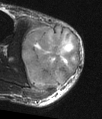
MRI of an extremity soft-tissue mass, one axial slice. Position 26 of 48 along the scan axis. T2-weighted fat-saturated. MR volume resampled by the dataset authors to the PET/CT grid (not the native acquisition matrix). 3.27 mm slice thickness. 102 × 119 image matrix, field of view 100 × 116 mm. Male patient. From the clinical record (not read from this slice): histological type: pleiomorphic liposarcoma; grade: high; site of the primary tumour: right calf.
Outlined on this slice (expert contour drawn on MRI and transferred to this co-registered scan by the dataset authors):
- gross tumour volume including surrounding oedema: bounding box [x1, y1, x2, y2] px = [21, 21, 81, 95]
- gross tumour volume (mass): [21, 26, 81, 88]